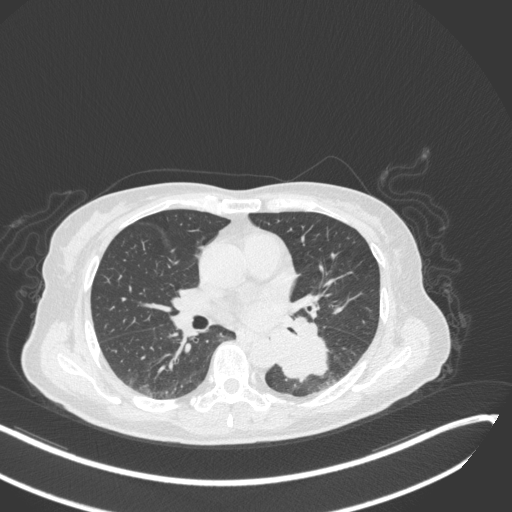
Chest CT, one axial slice. Position 143 of 342 along the scan axis. Reconstruction kernel B31f. Lung window (W 1500 / L -600 HU). 512 × 512 image matrix, field of view 400 × 400 mm. Patient: female, 64 years. From the clinical record (not read from this slice): clinical TNM (as recorded): T3 N1 M1; histopathological grade: G3.
Outlined on this slice (bounding box drawn by a radiologist):
- lung tumour (recorded histology: small cell carcinoma): box from (x=278, y=334) to (x=337, y=382) px